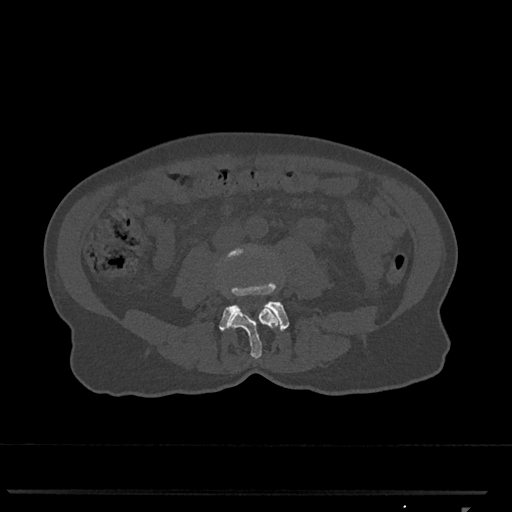
CT including the spine, one axial slice; position 240 of 793 along the scan axis; reconstruction kernel Br40s/3; bone window (W 1800 / L 400 HU); 512 × 512 image matrix. Female patient, age 62 years. From the clinical record (not read from this slice): primary cancer: renal.
Outlined on this slice (semi-automatically segmented with operator editing):
- L3 vertebra: box from (x=226, y=248) to (x=280, y=359) px
- L4 vertebra: (x=219, y=282)–(x=289, y=332)